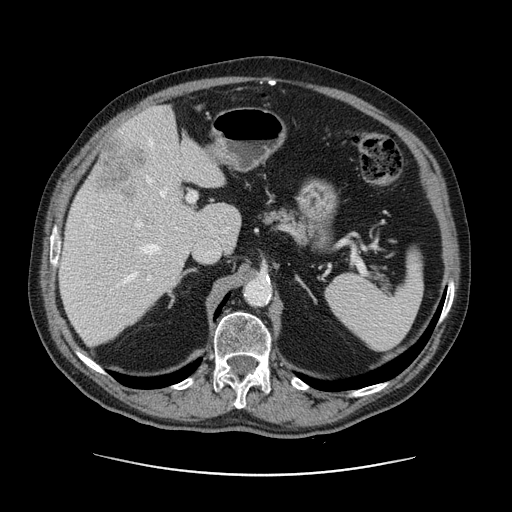
Contrast-enhanced abdominal CT, one axial slice. Slice 81 of 141 in the series (ordered by position). 120 kVp. Soft-tissue window (W 400 / L 40 HU). 512 × 512 image matrix. Male patient, age 72 years. From the clinical record (not read from this slice): diagnosis: colorectal cancer liver metastases, imaged before liver resection; multiple liver metastases: yes.
Structures marked on this image (outlined manually by an expert reader):
- hepatic veins: bounding box [x1, y1, x2, y2] px = [124, 139, 167, 283]
- liver: [59, 106, 241, 345]
- planned liver remnant (the part of the liver to remain after resection): [59, 135, 241, 346]
- portal vein (with intrahepatic branches): [86, 192, 197, 287]
- liver metastasis: [95, 142, 148, 199]